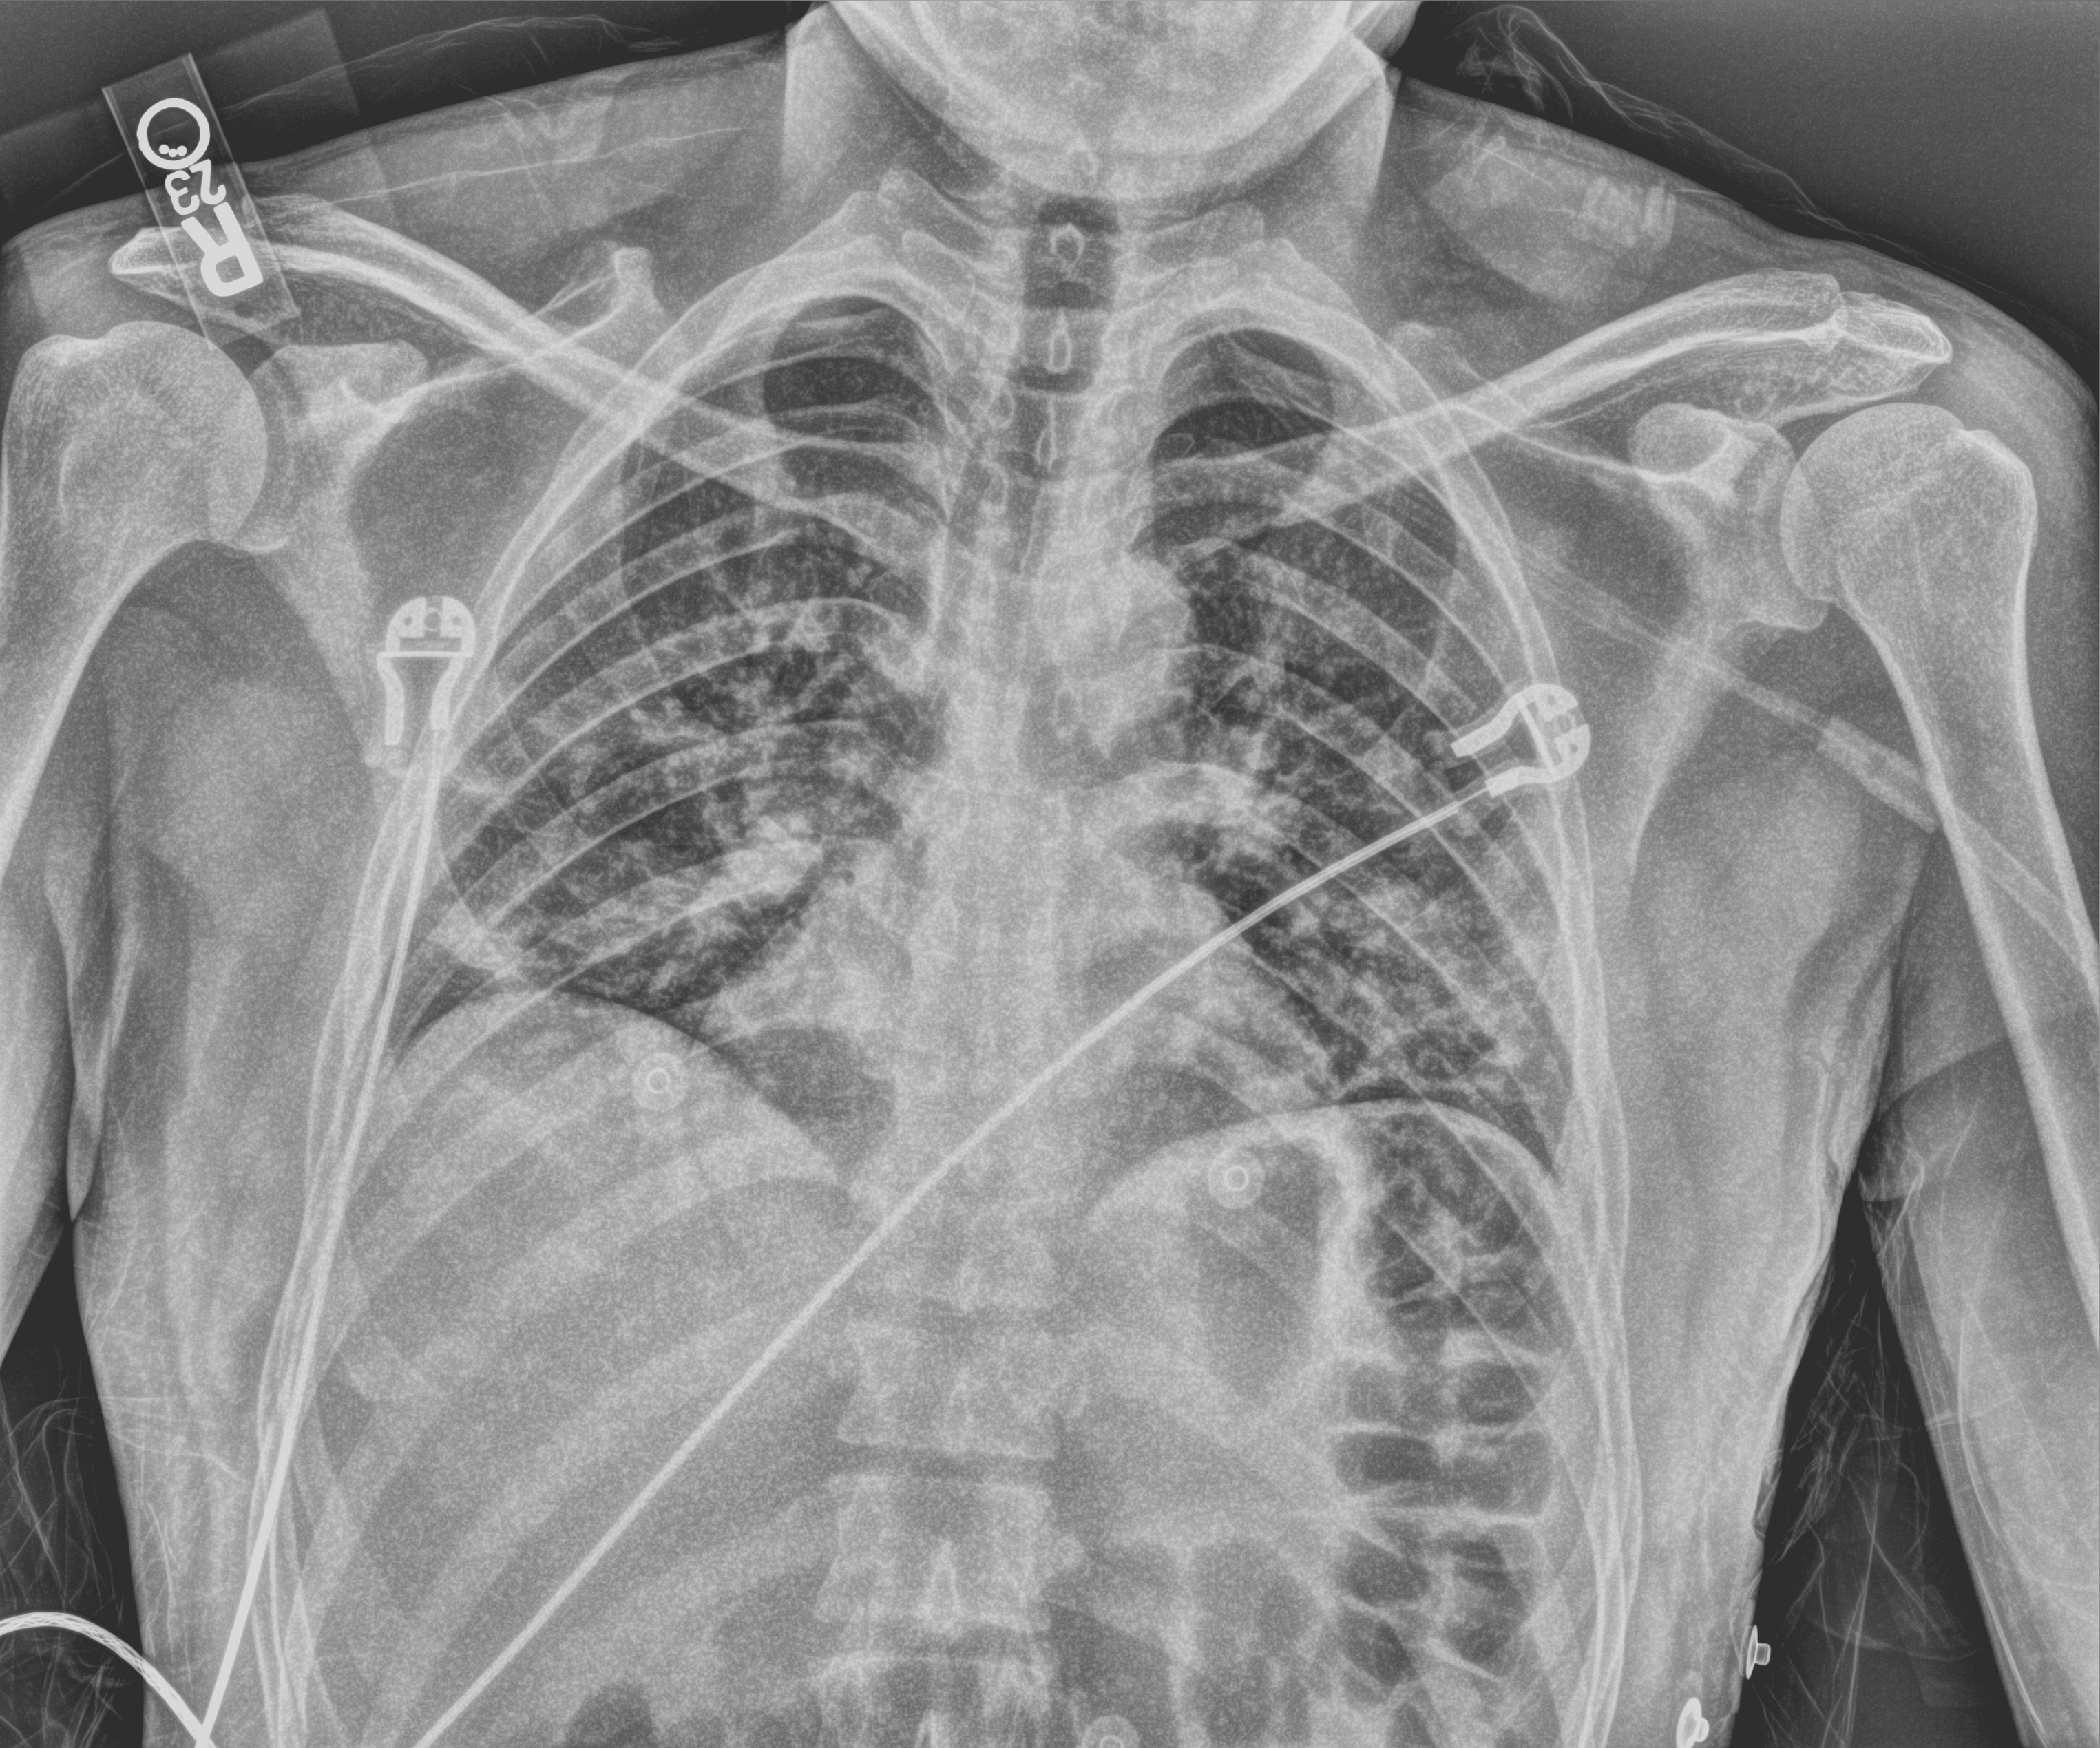
Portable chest radiograph, anteroposterior (AP) projection. Male patient hospitalised with COVID-19, age 18–59 years.
Hospital-stay facts (about this admission, not read from this image; timing relative to this image not recorded): admitted to intensive care during this hospital stay: yes; mechanically ventilated during this hospital stay: no; smoking status (admission record): never.